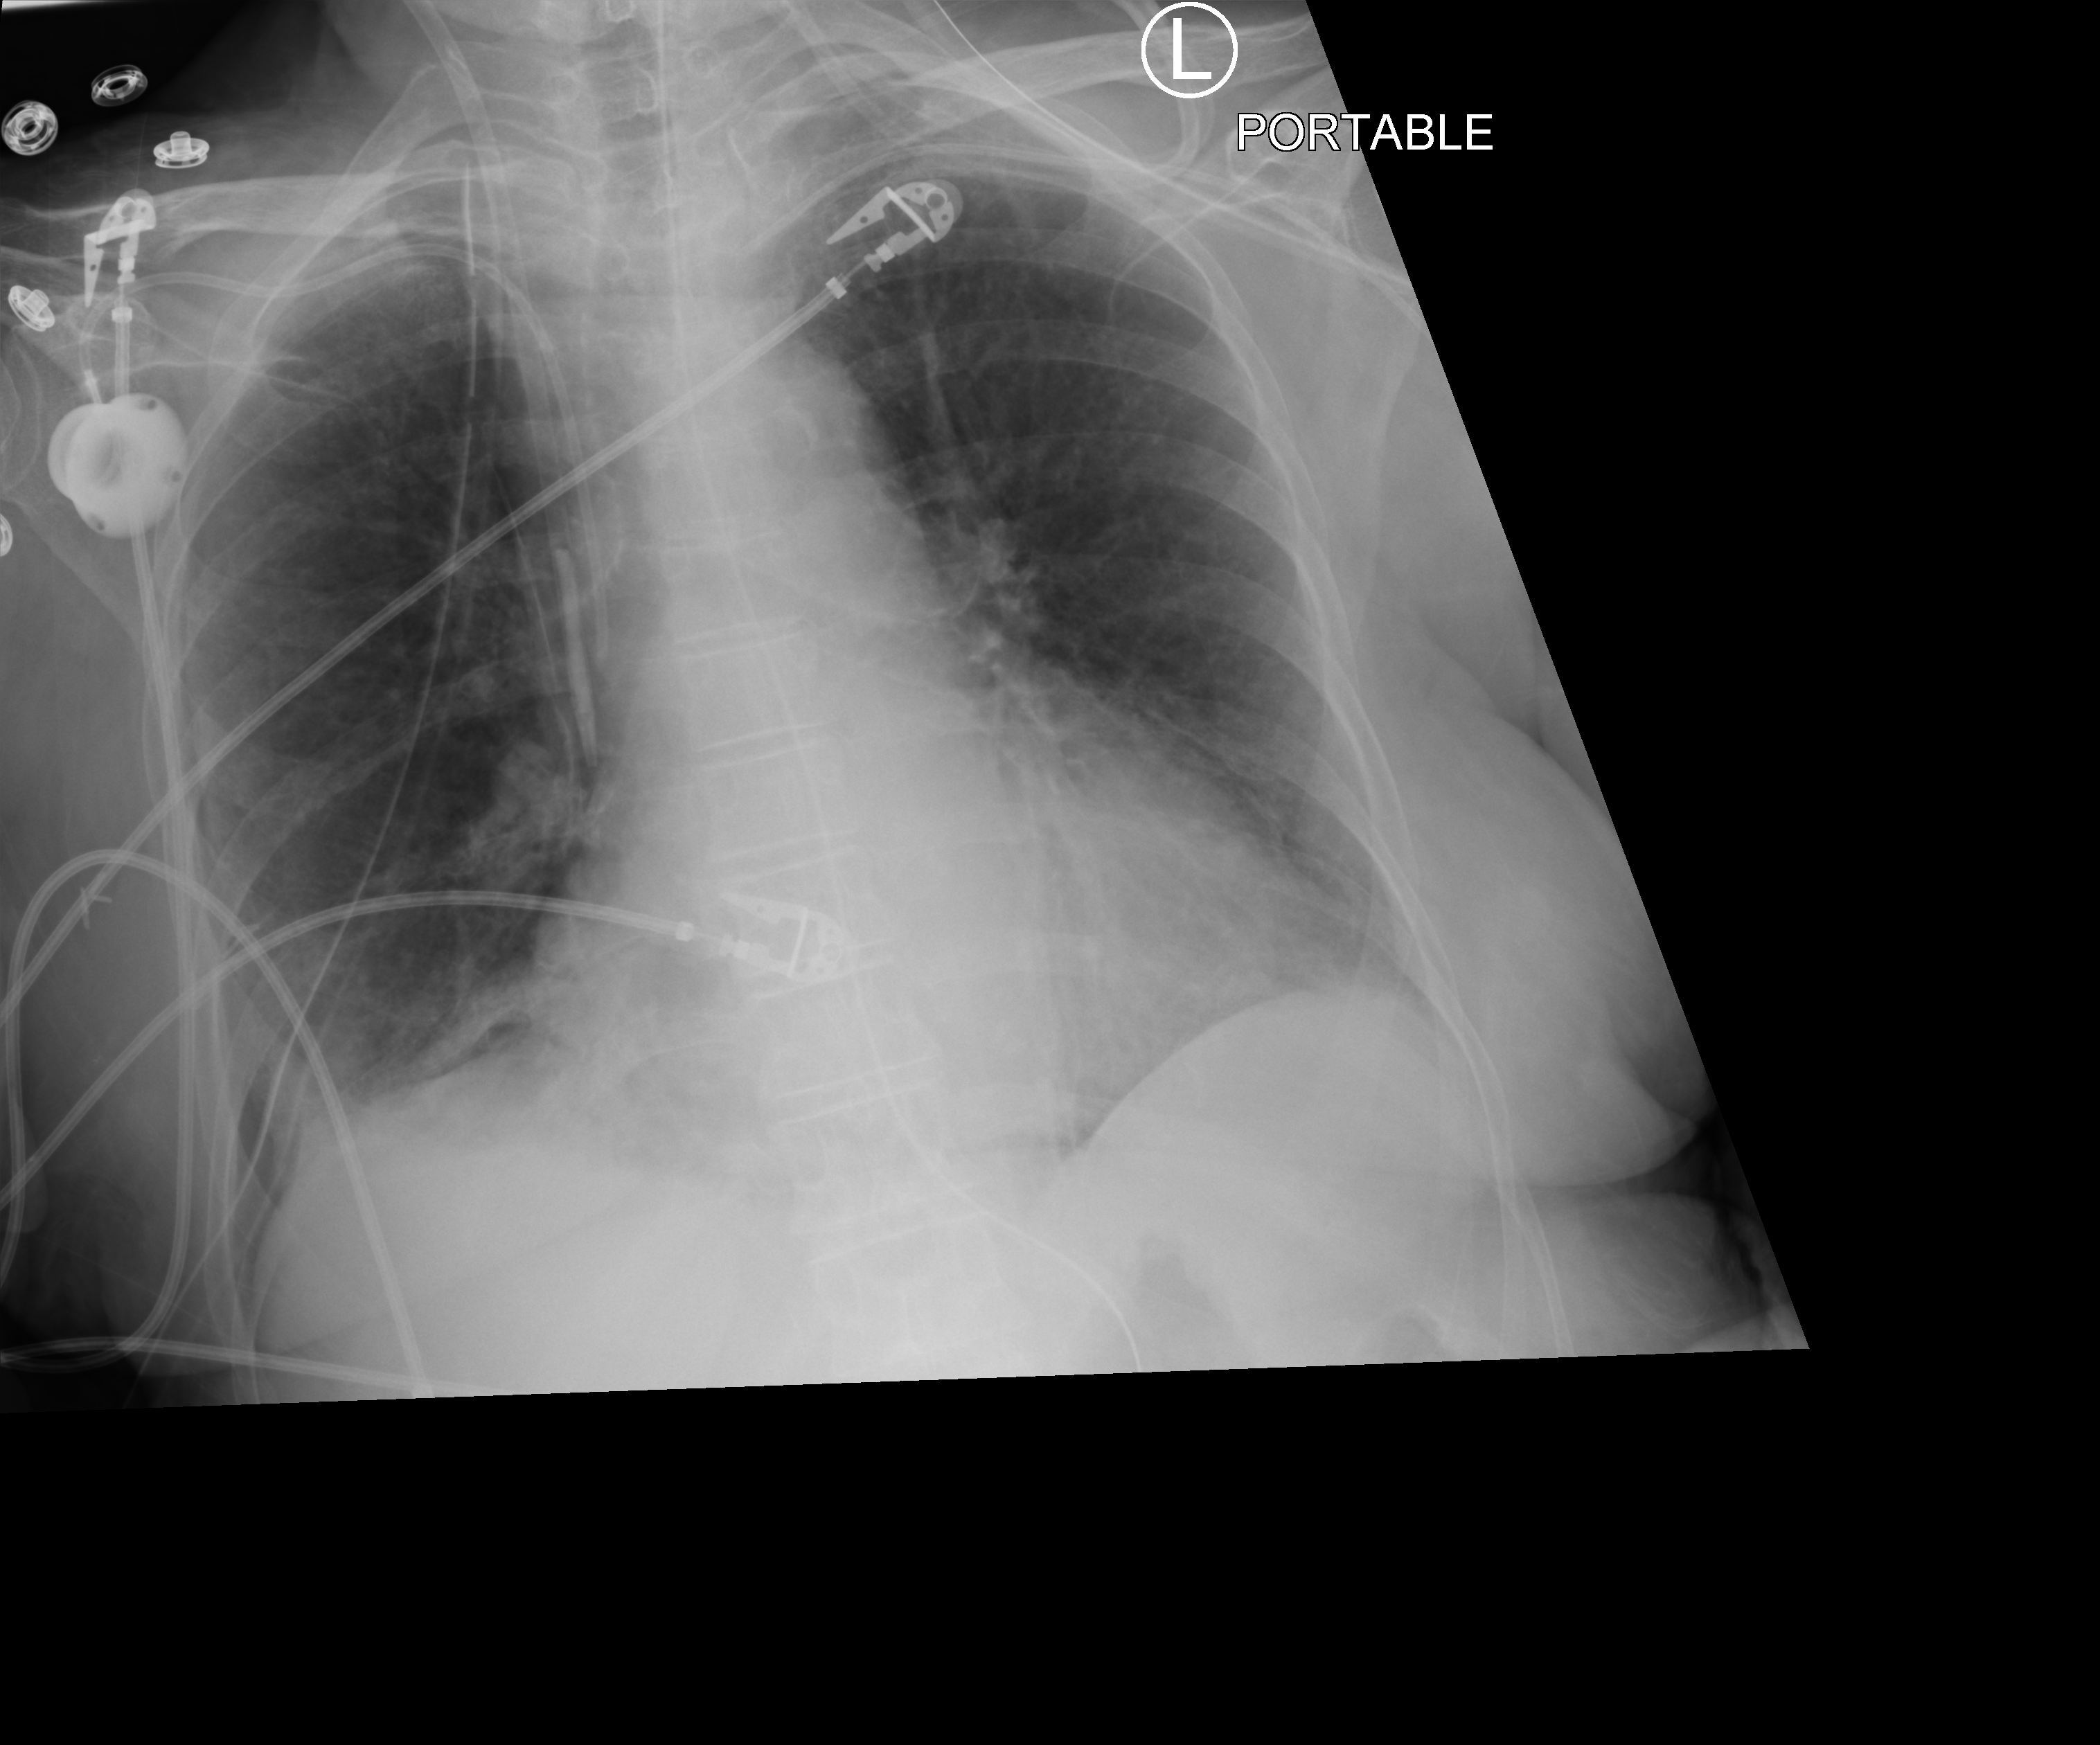
Portable chest radiograph; anteroposterior (AP) projection. Patient hospitalised with COVID-19; female, aged 60–74 years.
From the hospital-stay record, not from the radiograph (when in the stay this image was taken is not recorded):
- length of hospital stay: 43 days
- admitted to intensive care during this hospital stay: yes
- mechanically ventilated during this hospital stay: yes